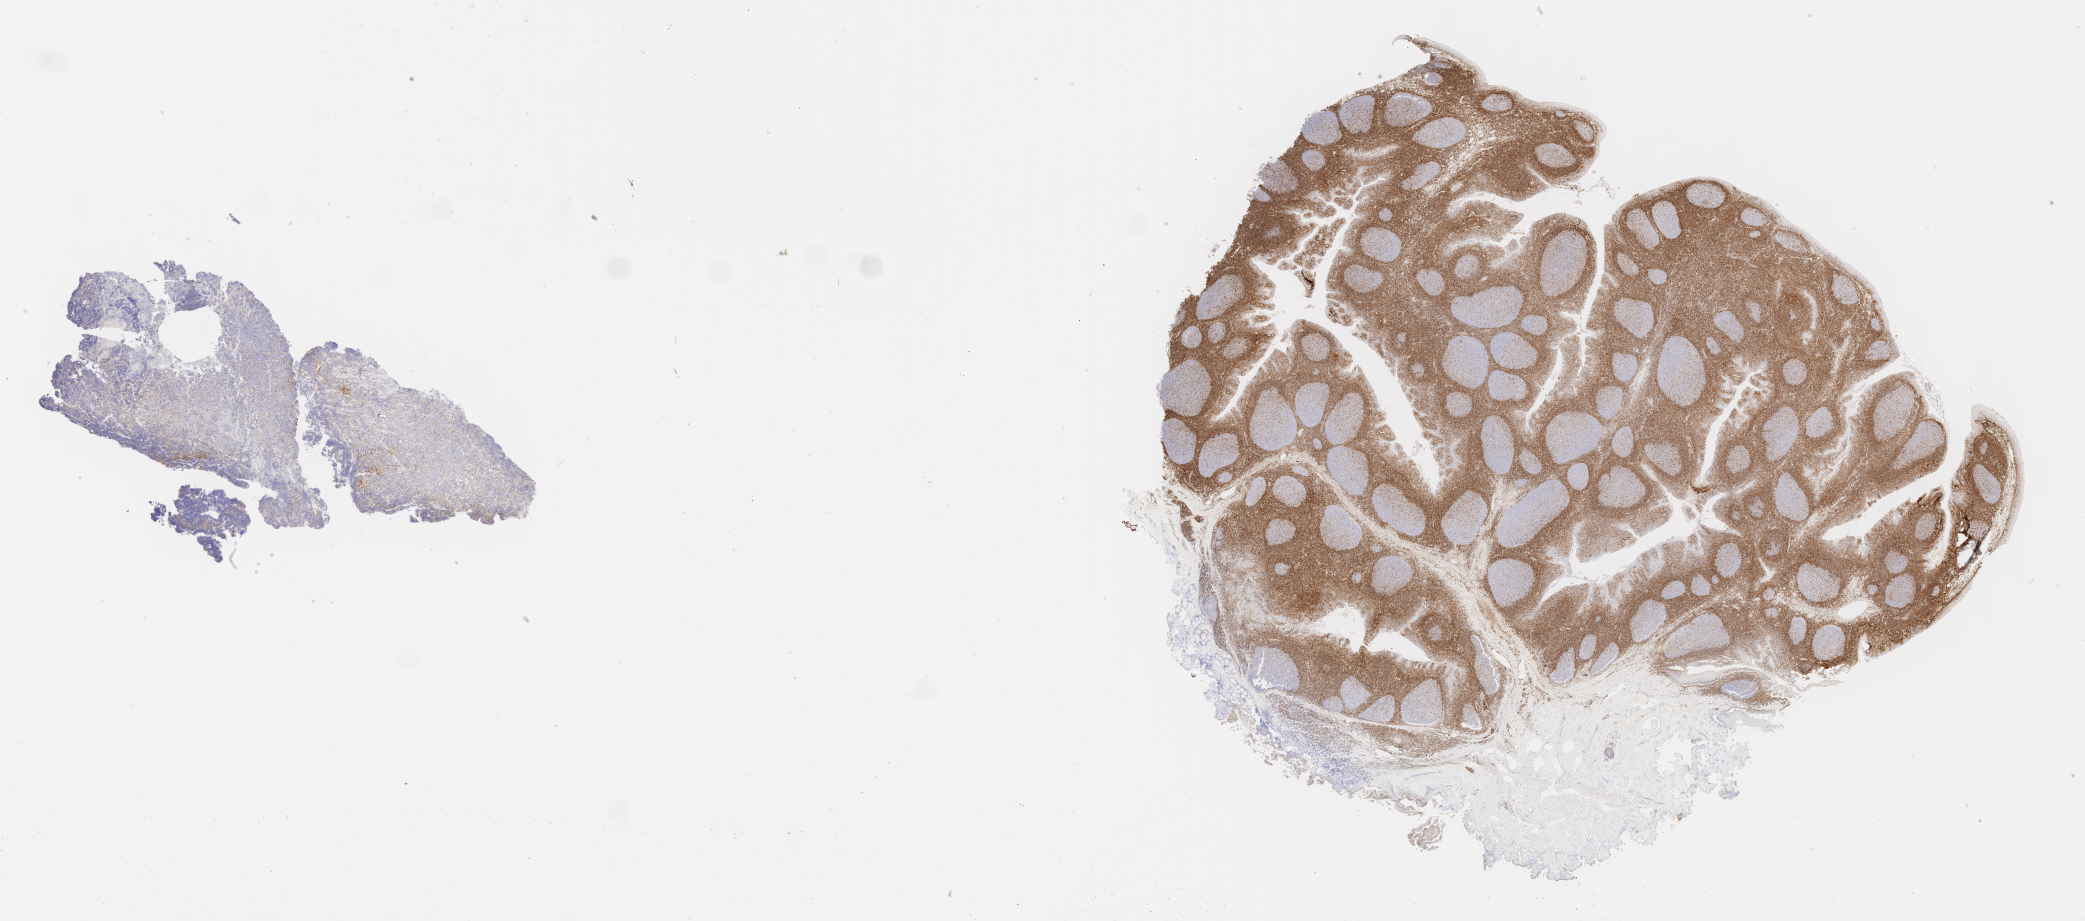
IHC for BCL2, whole-slide image, a low-resolution overview of the entire scanned area, about 33.7 x 14.9 mm, specimen: tumor tissue, site: mandible. Patient: male, age 25 years.
• diagnosis: Diffuse large B-cell lymphoma, NOS